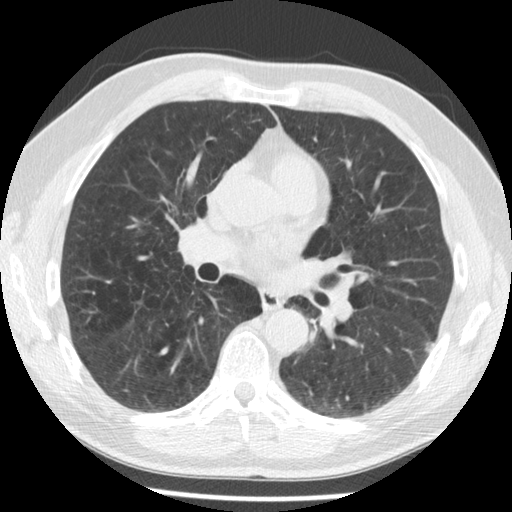
Chest CT (low-dose screening protocol), one axial image; second screening round (one year after baseline); lung window (W 1500 / L -600 HU); 2.5 mm slice thickness; standard (soft-tissue) reconstruction kernel (STANDARD); 120 kVp. Male participant, aged 57 years at enrolment. Former smoker at enrolment.
Expert-annotated lung lesion, bounding box <415,330,445,364> (left, top, right, bottom; pixels). Reader record for this screening exam (exam-level; its link to the box is not recorded): non-calcified nodule or mass ≥4 mm, left lower lobe, 6 × 5 mm, poorly defined margins, soft tissue attenuation, pre-existing on the prior screen: yes; interval growth: no. Official screen result: positive, no significant change: stable abnormalities potentially related to lung cancer, unchanged since the prior screening exam. Participant outcome: lung cancer diagnosed 427 days after this screen — non-small cell carcinoma, left lower lobe, stage IV (AJCC 6th edition), 13 mm at pathology.